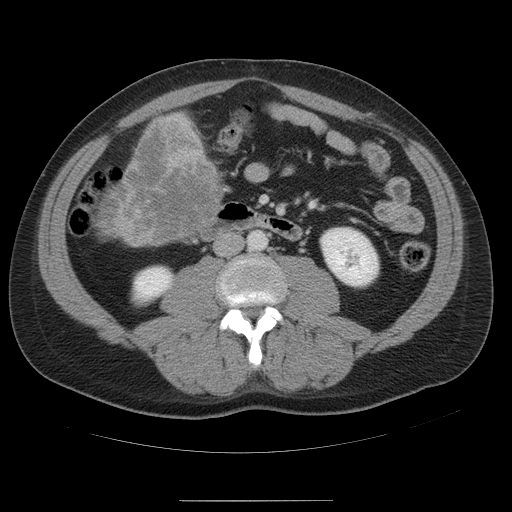
Contrast-enhanced abdominal CT, one axial slice; position 10 of 54 along the scan axis; intravenous contrast given; soft-tissue window (W 400 / L 40 HU); 5 mm slice thickness; 512 × 512 image matrix, field of view 436 × 436 mm. Male patient, age 40 years. Case-level facts recorded for this patient, not image findings: diagnosis: colorectal cancer liver metastases, imaged before liver resection; multiple liver metastases: no; largest metastasis: 15 cm.
Structures marked on this image (manually delineated by an expert):
- liver: bounding box (x1, y1, x2, y2) in pixels: (98, 113, 224, 247)
- liver metastasis: (98, 117, 225, 245)